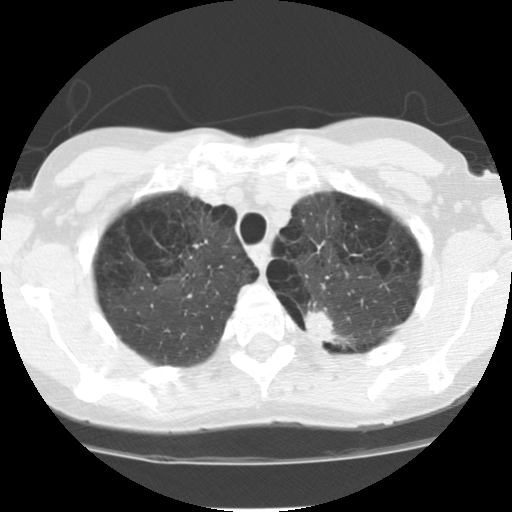
Low-dose screening chest CT, one axial slice; lung window (W 1500 / L -600 HU); 512 × 512 image matrix, field of view 300 × 300 mm.
Annotated regions visible in this slice (outlined manually by an expert reader):
- lesion 1 (tumor, upper lobe of left lung): bounding box <305,310,343,344> (left, top, right, bottom; pixels)